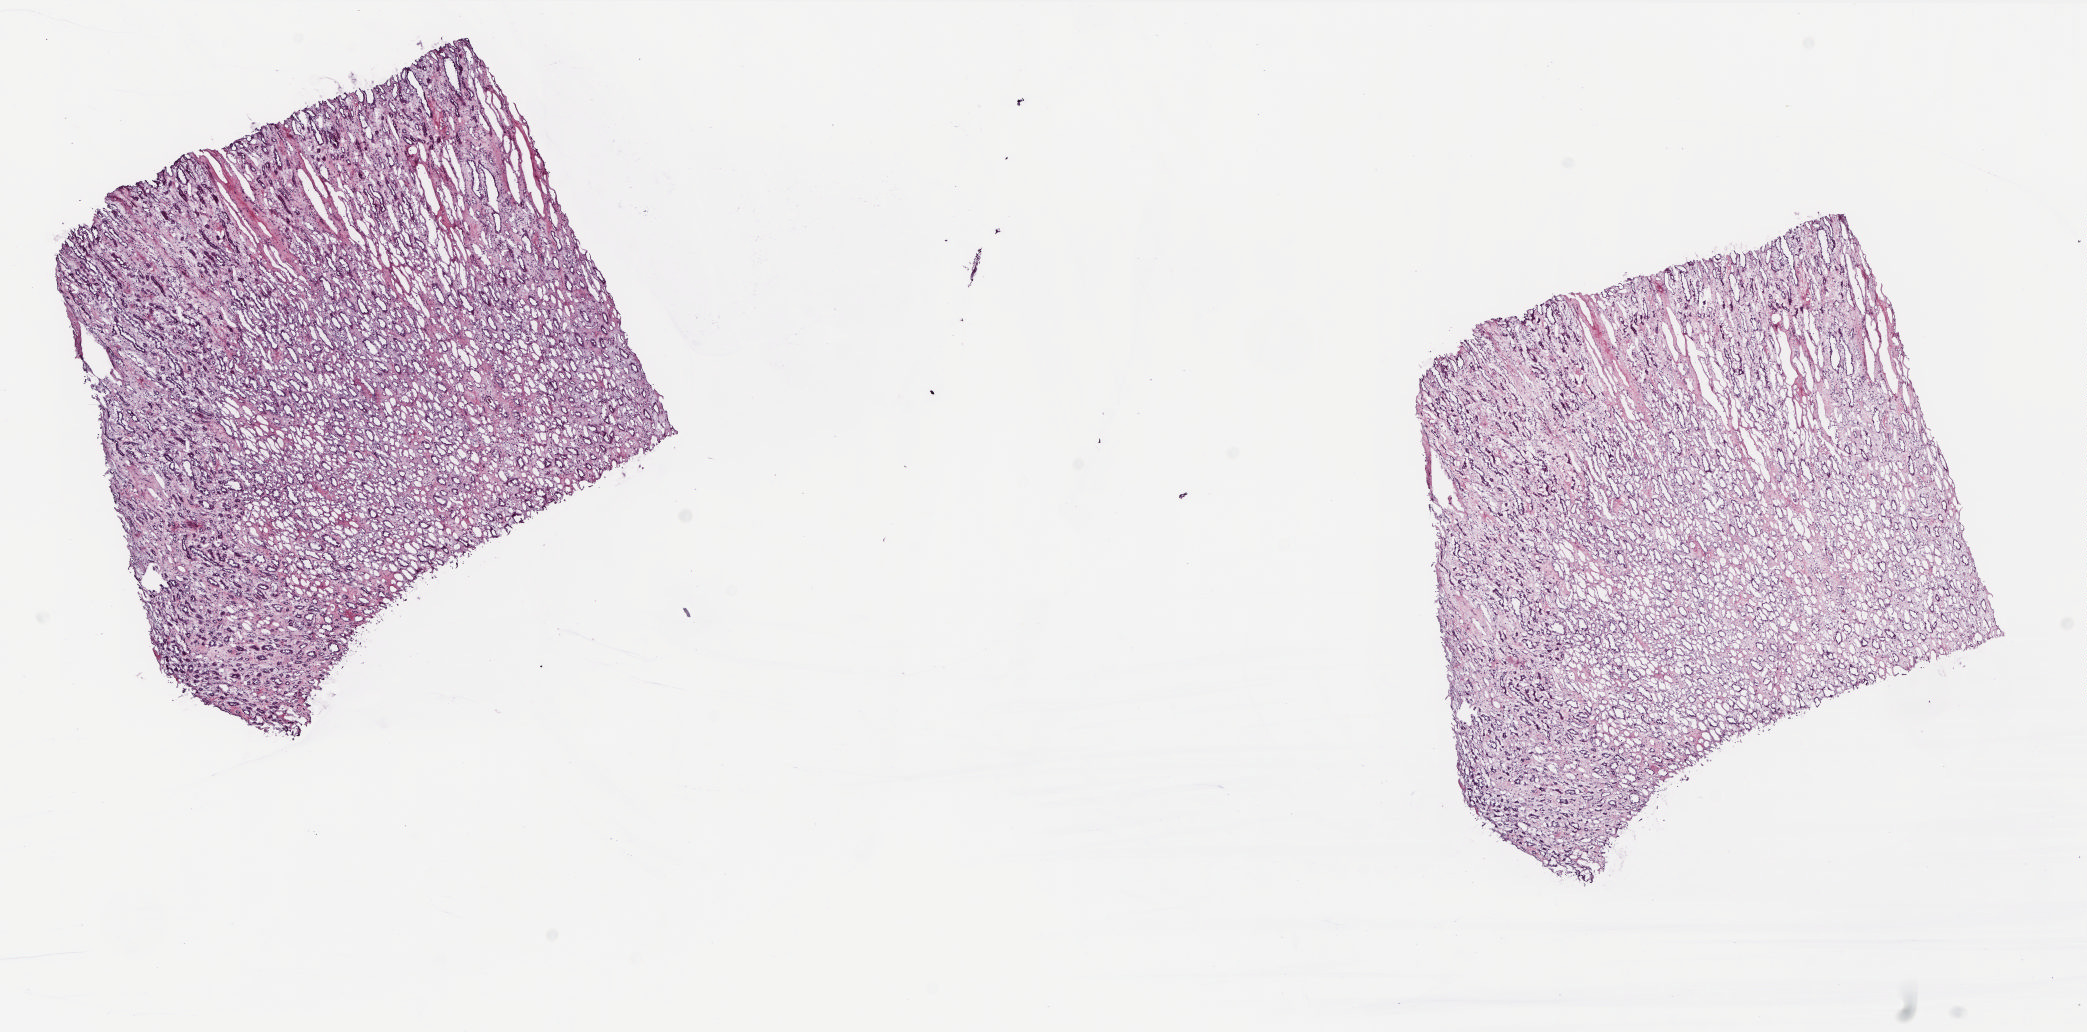
Whole-slide histology image, H&E-stained, low-resolution overview of the scanned area, about 16.8 x 8.3 mm (acquisition: 20x scan). Frozen section from the top of the tissue portion. Solid tissue normal (non-tumour tissue) sample from the kidney. Male patient; age at initial diagnosis 74 years. Composition of this section per pathologist review: tumour cells 0%, tumour nuclei 0%, normal cells 100%, stromal cells 0%, necrosis 0%. Inflammatory infiltration, as recorded: lymphocyte infiltration 2%, monocyte infiltration 2%, neutrophil infiltration 0%.
This section: solid tissue normal (non-tumour) sample from the same patient. Patient diagnosis: Renal cell carcinoma, chromophobe type.